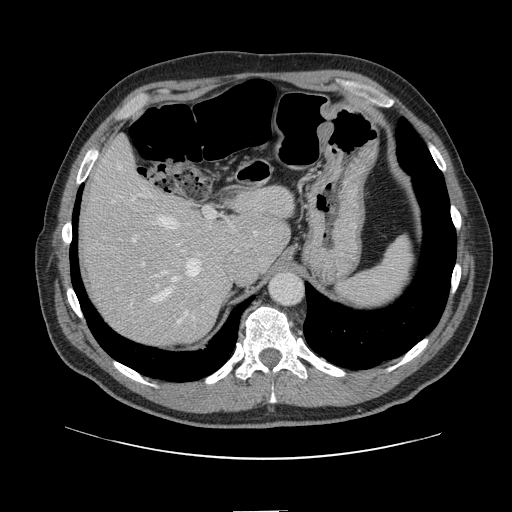
Contrast-enhanced abdominal CT, one axial slice; position 102 of 161 along the scan axis; intravenous contrast given; soft-tissue window (W 400 / L 40 HU); 512 × 512 image matrix, field of view 412 × 412 mm. Male patient, age 66 years. Case-level facts recorded for this patient, not image findings: diagnosis: colorectal cancer liver metastases, imaged before liver resection; multiple liver metastases: no; largest metastasis: 3.5 cm; disease in both lobes: no.
Structures marked on this image (expert manual segmentation):
- hepatic veins: bounding box <113,165,202,313> (left, top, right, bottom; pixels)
- liver: <82,142,293,345>
- planned liver remnant (the part of the liver to remain after resection): <82,142,293,308>
- portal vein (with intrahepatic branches): <130,209,216,307>
- liver metastasis: <196,296,206,306>